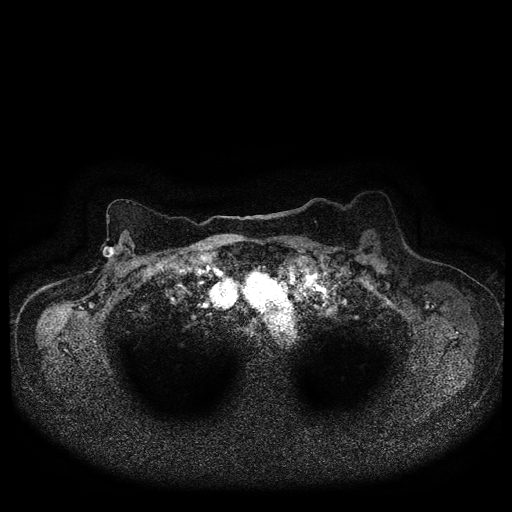
Breast MRI (dynamic contrast-enhanced, multi-phase), one axial slice; position 74 of 116 along the scan axis; dynamic contrast-enhanced series, time point 2 of 5 at this slice position (early post-contrast); 1.5 T; TE 2.7 ms, TR 5.4 ms; 512 × 512 image matrix, field of view 340 × 340 mm. Patient: female, 72 years.
Structures marked on this image (semi-automatic segmentation, software-assisted and operator-edited):
- breast lesion (labelled 'tumour' in the annotation; benign lesions carry a separate 'benign' label): box from (x=101, y=245) to (x=117, y=259) px